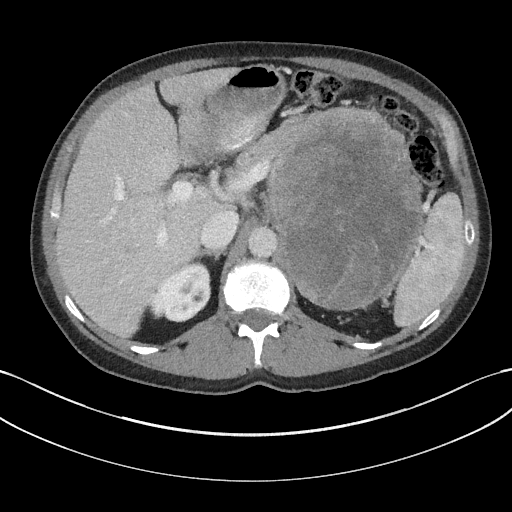
Contrast-enhanced abdominal CT, one axial slice; reconstruction kernel I31f/3; 100 kVp; intravenous contrast given; soft-tissue window (W 400 / L 40 HU); 3 mm slice thickness; 512 × 512 image matrix, field of view 384 × 384 mm. Patient: male, 58 years. Case-level facts recorded for this patient, not image findings: diagnosis: adrenocortical carcinoma; tumour side: left adrenal; tumour size at pathology: 22 cm; Ki-67 index: 26 %; stage (as recorded): 2.
Annotated regions visible in this slice (semi-automatically segmented with operator editing):
- mass: bounding box <271,121,420,306> (left, top, right, bottom; pixels)